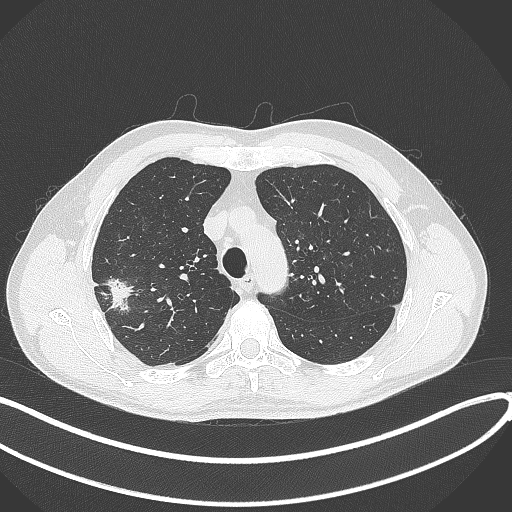
Chest CT, one axial slice; position 315 of 381 along the scan axis; 120 kVp; lung window (W 1500 / L -600 HU); 512 × 512 image matrix. Male patient, age 62 years. Case-level facts recorded for this patient, not image findings: clinical TNM (as recorded): T1c N0 M0.
Annotated regions visible in this slice (rectangle marked by the reading radiologist):
- lung tumour (recorded histology: adenocarcinoma): bounding box <101,275,135,312> (left, top, right, bottom; pixels)